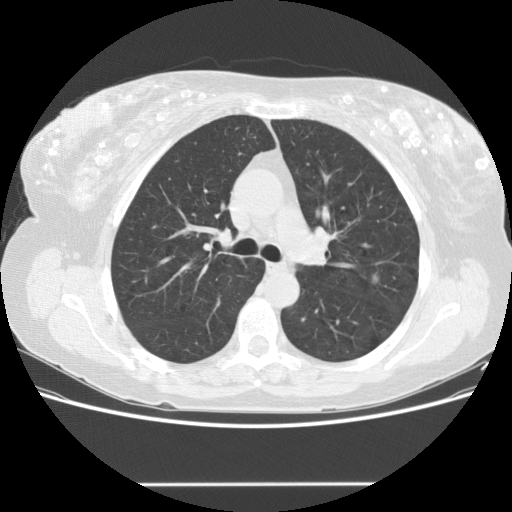
Low-dose screening chest CT, one axial slice; position 100 of 151 along the scan axis; reconstruction kernel STANDARD; 120 kVp; lung window (W 1500 / L -600 HU); 2.5 mm slice thickness; 512 × 512 image matrix.
Structures marked on this image (manually delineated by an expert):
- lesion 1 (tumor, upper lobe of left lung): box from (x=373, y=275) to (x=378, y=281) px